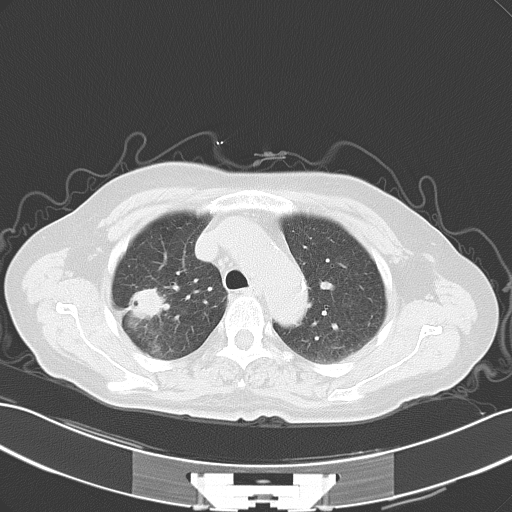
Chest CT, one axial slice; slice 43 of 57 in the series (ordered by position); reconstruction kernel B70f; 120 kVp; lung window (W 1500 / L -600 HU); 5 mm slice thickness; 512 × 512 image matrix, field of view 353 × 353 mm. Patient: female, 65 years. From the clinical record (not read from this slice): clinical TNM (as recorded): T1c N0 M1c.
Structures marked on this image (rectangle marked by the reading radiologist):
- lung tumour (recorded histology: adenocarcinoma): bounding box [x1, y1, x2, y2] px = [129, 283, 172, 328]